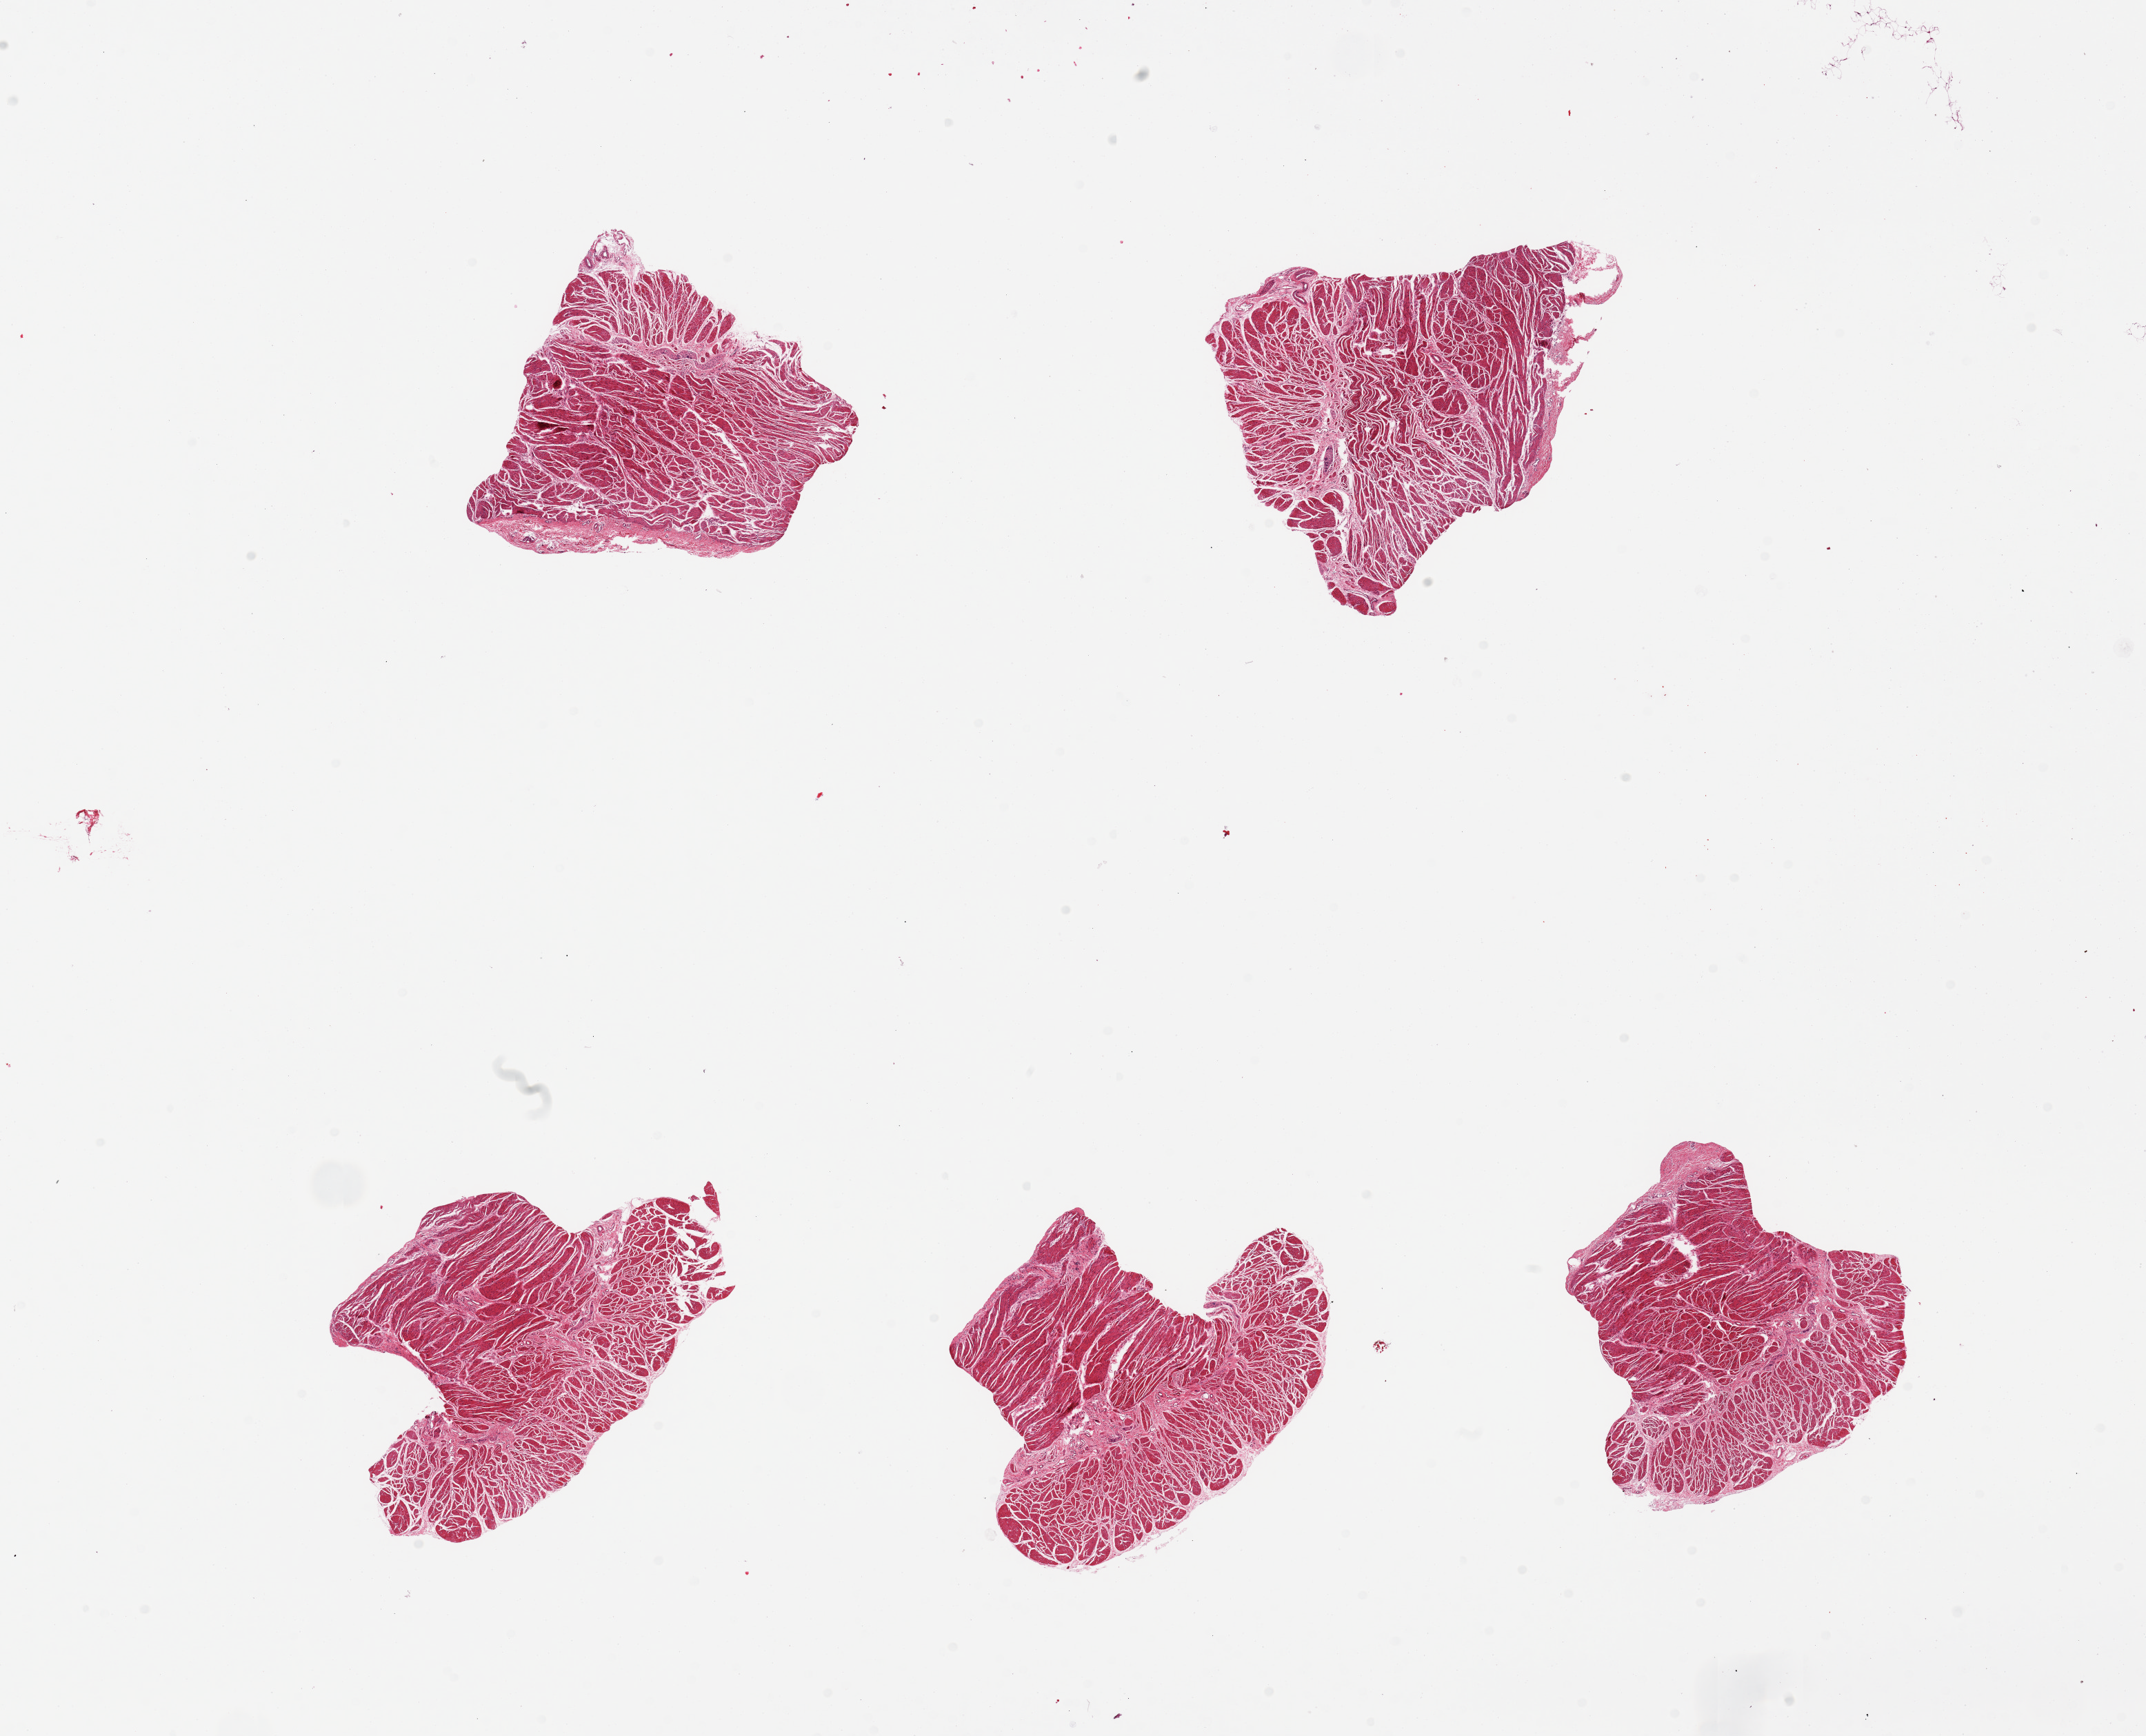
Digitized haematoxylin and eosin-stained section, whole scanned area (about 24.6 x 19.9 mm) shown as a low-resolution overview. PAXgene-fixed, paraffin-embedded tissue. Target tissue: esophageal muscle. Tissue donor sample. Male donor.
* review note (as recorded): 5 pieces, all muscularis